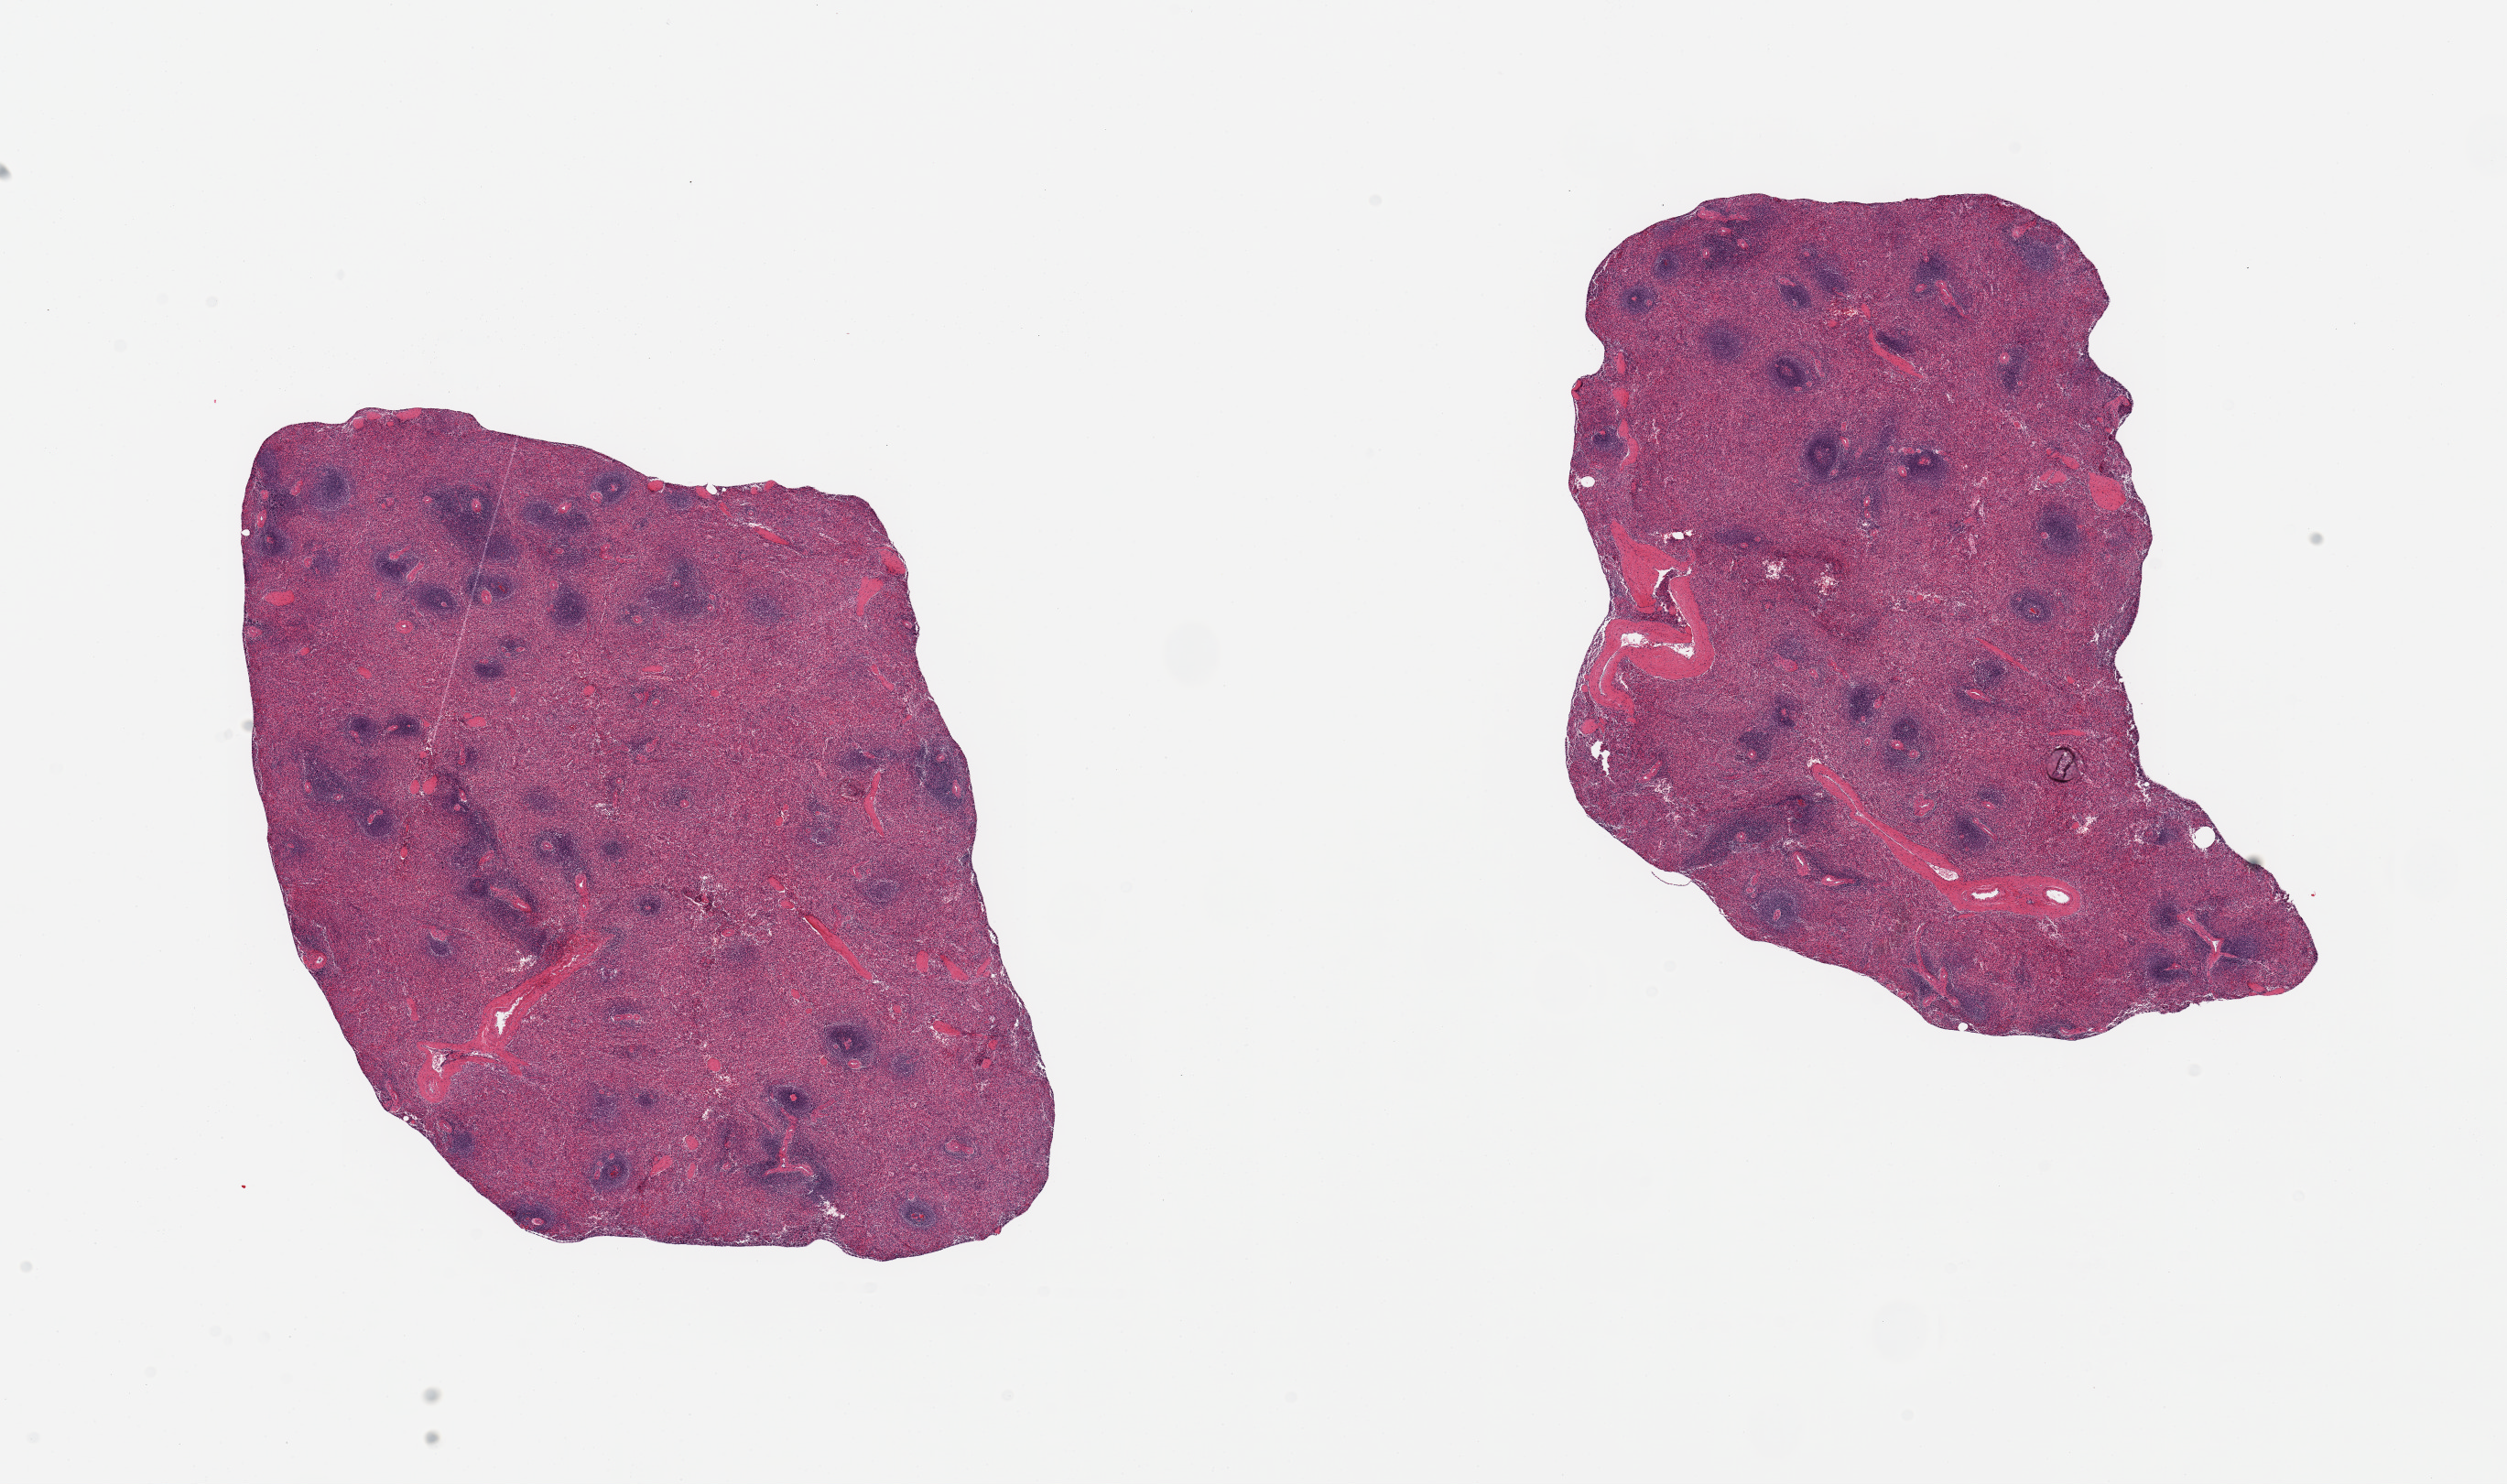
Whole-slide image, H&E stain — low-resolution overview of the scanned area, about 21.7 x 12.8 mm, PAXgene-fixed paraffin-embedded (PFPE) section, section of spleen (target tissue), tissue donor sample. Donor: female.
Pathologist's review note for this sample: 2 pieces; not congested.